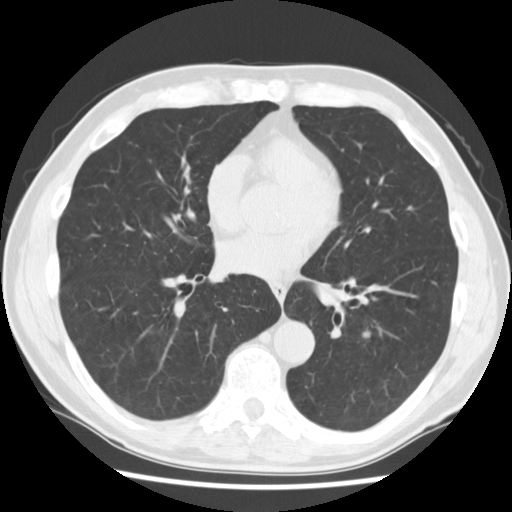
Low-dose screening chest CT, axial slice, first (baseline) screen, lung window (W 1500 / L -600 HU), 2.5 mm slice thickness, standard (soft-tissue) reconstruction kernel (STANDARD), slice 117 of 269 in the series. Male, age 64 years at enrolment.
• Expert-annotated lung lesion, box from (x=351, y=320) to (x=382, y=347) px.
• No non-calcified nodule or mass ≥4 mm was recorded by the screening reader at this exam.
• Participant outcome: lung cancer diagnosed 928 days after this screen — adenocarcinoma, NOS, left lower lobe, stage IV (AJCC 6th edition), 44 mm at pathology.